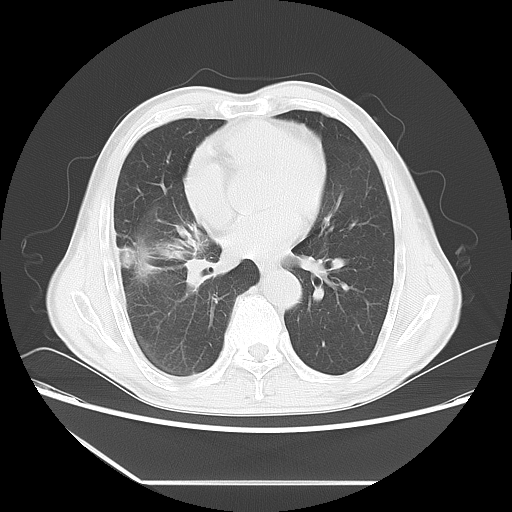
Chest CT, one axial slice; reconstruction kernel LUNG; lung window (W 1500 / L -600 HU); 512 × 512 image matrix, field of view 386 × 386 mm. Patient: male, 72 years. Case-level facts recorded for this patient, not image findings: clinical TNM (as recorded): T1c N0 M0.
Annotated regions visible in this slice (rectangle marked by the reading radiologist):
- lung tumour (recorded histology: squamous cell carcinoma): bounding box [x1, y1, x2, y2] px = [117, 233, 200, 286]